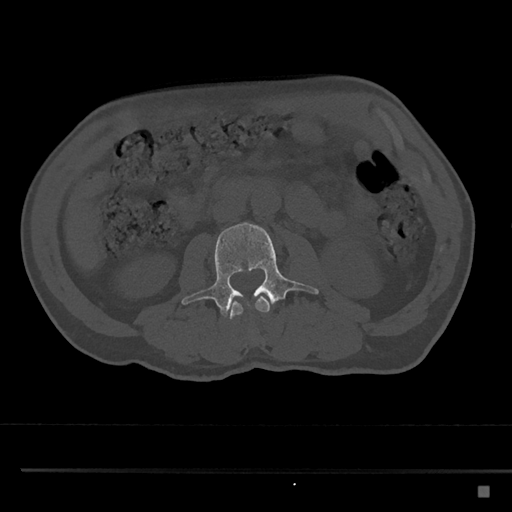
CT including the spine, one axial slice. Slice 710 of 797 in the series (ordered by position). Reconstruction kernel Br40s/3. 120 kVp. Bone window (W 1800 / L 400 HU). 0.5 mm slice thickness. 512 × 512 image matrix. Patient: male, 59 years. Case-level facts recorded for this patient, not image findings: primary cancer: prostate.
Structures marked on this image (semi-automatically segmented with operator editing):
- L2 vertebra: bounding box <227,296,270,319> (left, top, right, bottom; pixels)
- L3 vertebra: <181,222,319,316>